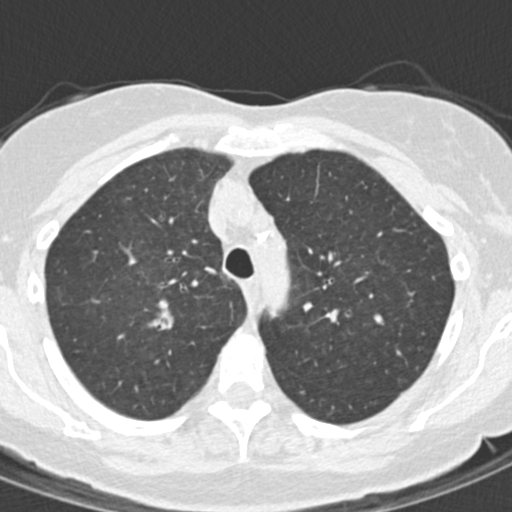
Low-dose screening chest CT, one axial slice. Slice 115 of 157 in the series (ordered by position). Reconstruction kernel B30f. 120 kVp. Lung window (W 1500 / L -600 HU). 2 mm slice thickness. 512 × 512 image matrix.
Annotated regions visible in this slice (expert manual segmentation):
- lesion 1 (tumor, upper lobe of right lung): bounding box [x1, y1, x2, y2] px = [147, 309, 174, 331]